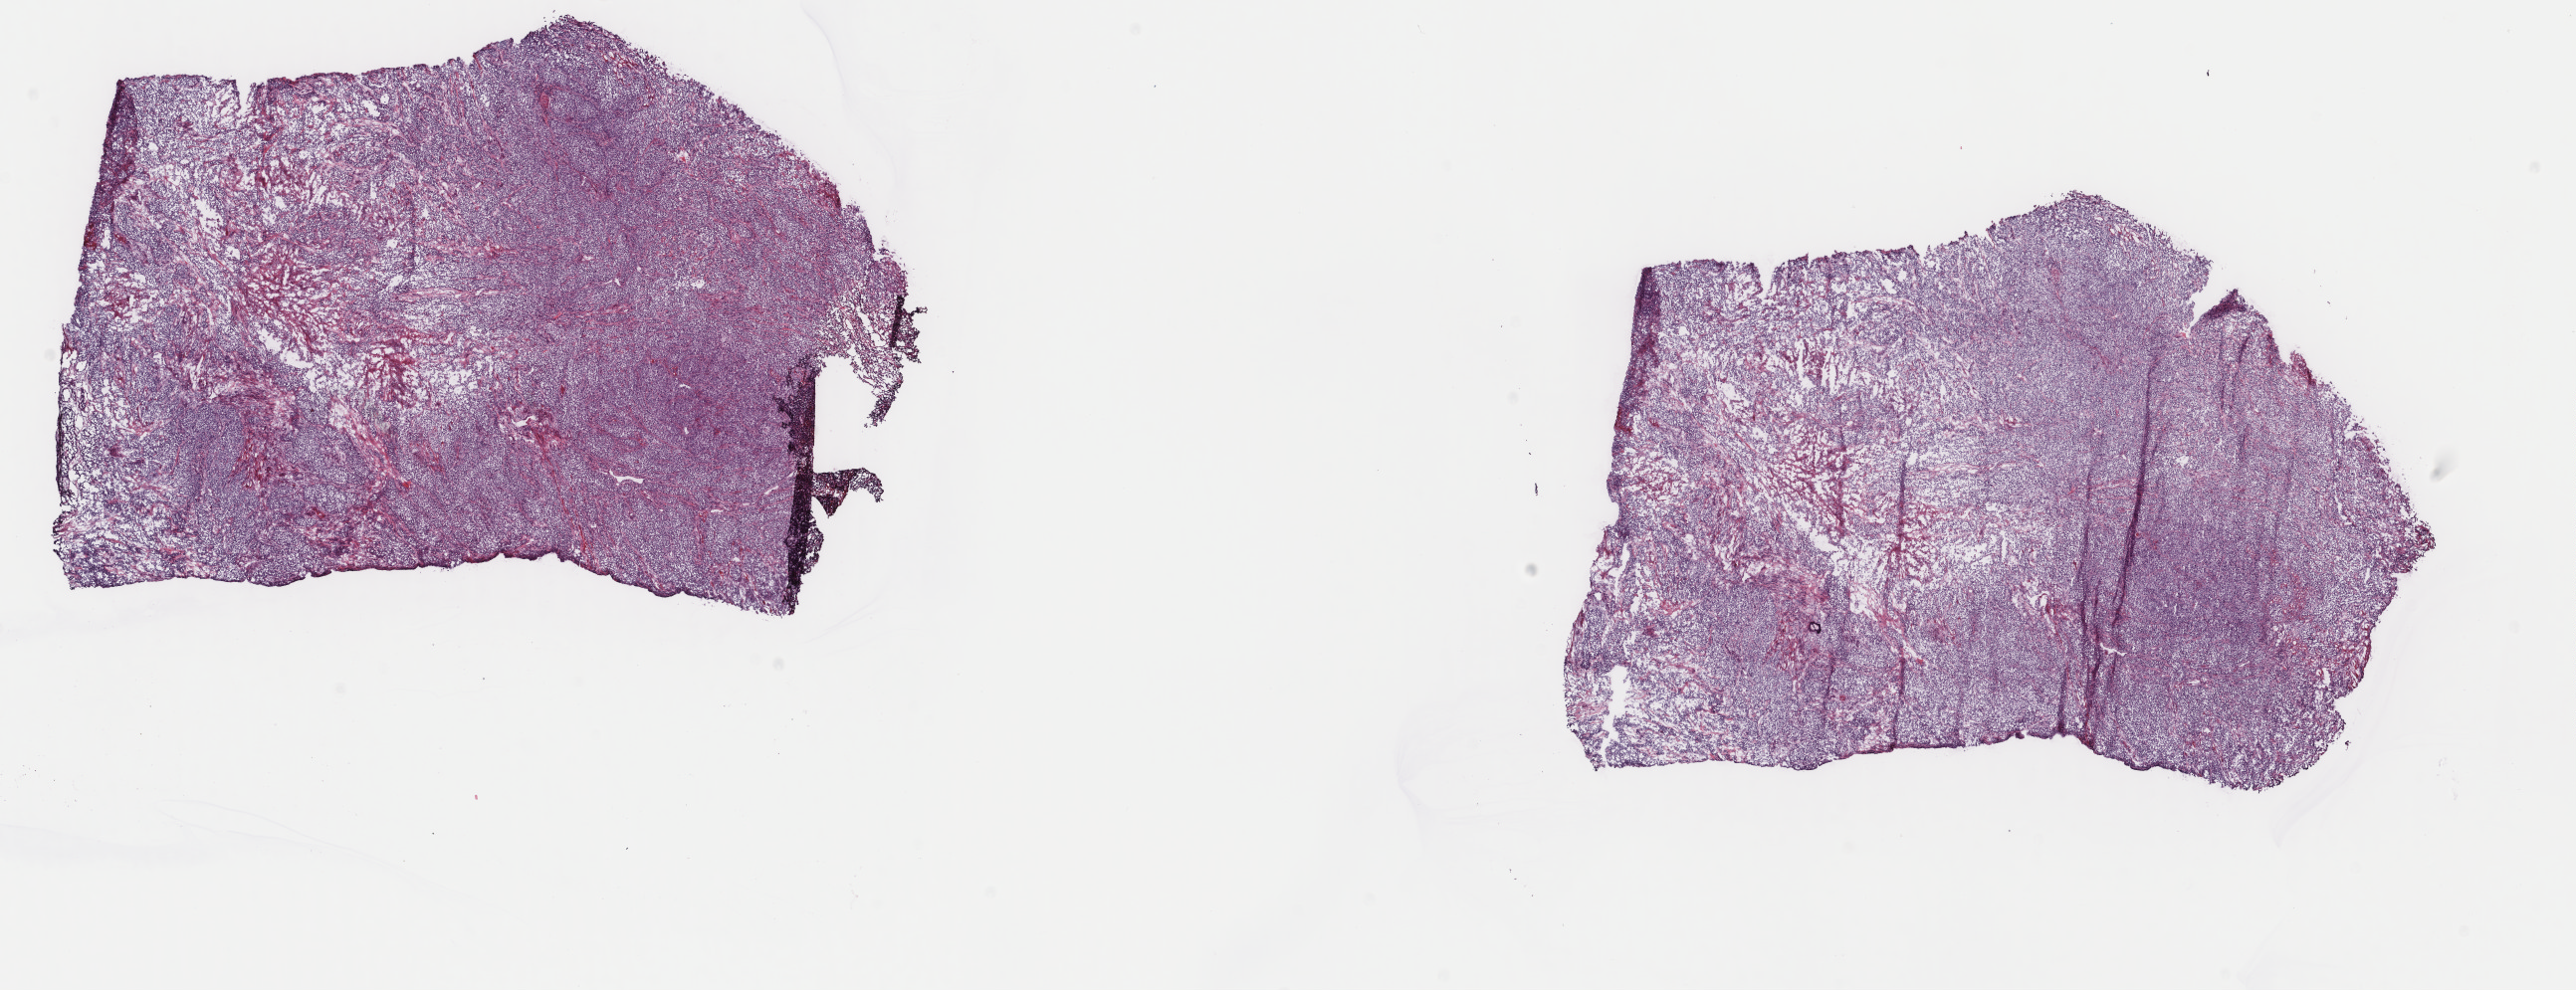
Digitized H&E tissue section (whole slide), shown as a low-resolution overview of the whole scanned area (about 20.5 x 7.9 mm). Frozen section from the top of the tissue portion. Head and neck, primary tumour sample. Patient: male, age at initial diagnosis 57 years. Histologic grade: G3 (poorly differentiated). Slide review estimates, as recorded: tumour cells 85%, tumour nuclei 90%, normal cells 0%, stromal cells 15%, necrosis 0%. Inflammatory infiltration, as recorded: lymphocyte infiltration 0%, monocyte infiltration 0%, neutrophil infiltration 0%.
Histologic diagnosis: Squamous cell carcinoma, NOS (tongue, NOS). AJCC pathologic stage: IVB (7th edition).